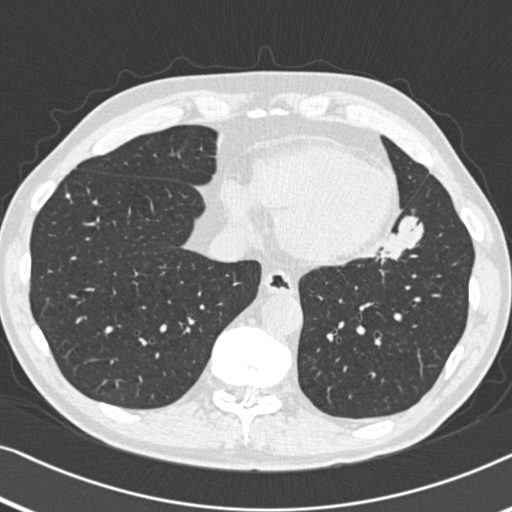
Low-dose screening chest CT, one axial slice; position 135 of 383 along the scan axis; reconstruction kernel B30f; 120 kVp; lung window (W 1500 / L -600 HU); 512 × 512 image matrix.
Outlined on this slice (expert manual segmentation):
- lesion 1 (tumor, upper lobe of left lung): bounding box <379,216,424,262> (left, top, right, bottom; pixels)